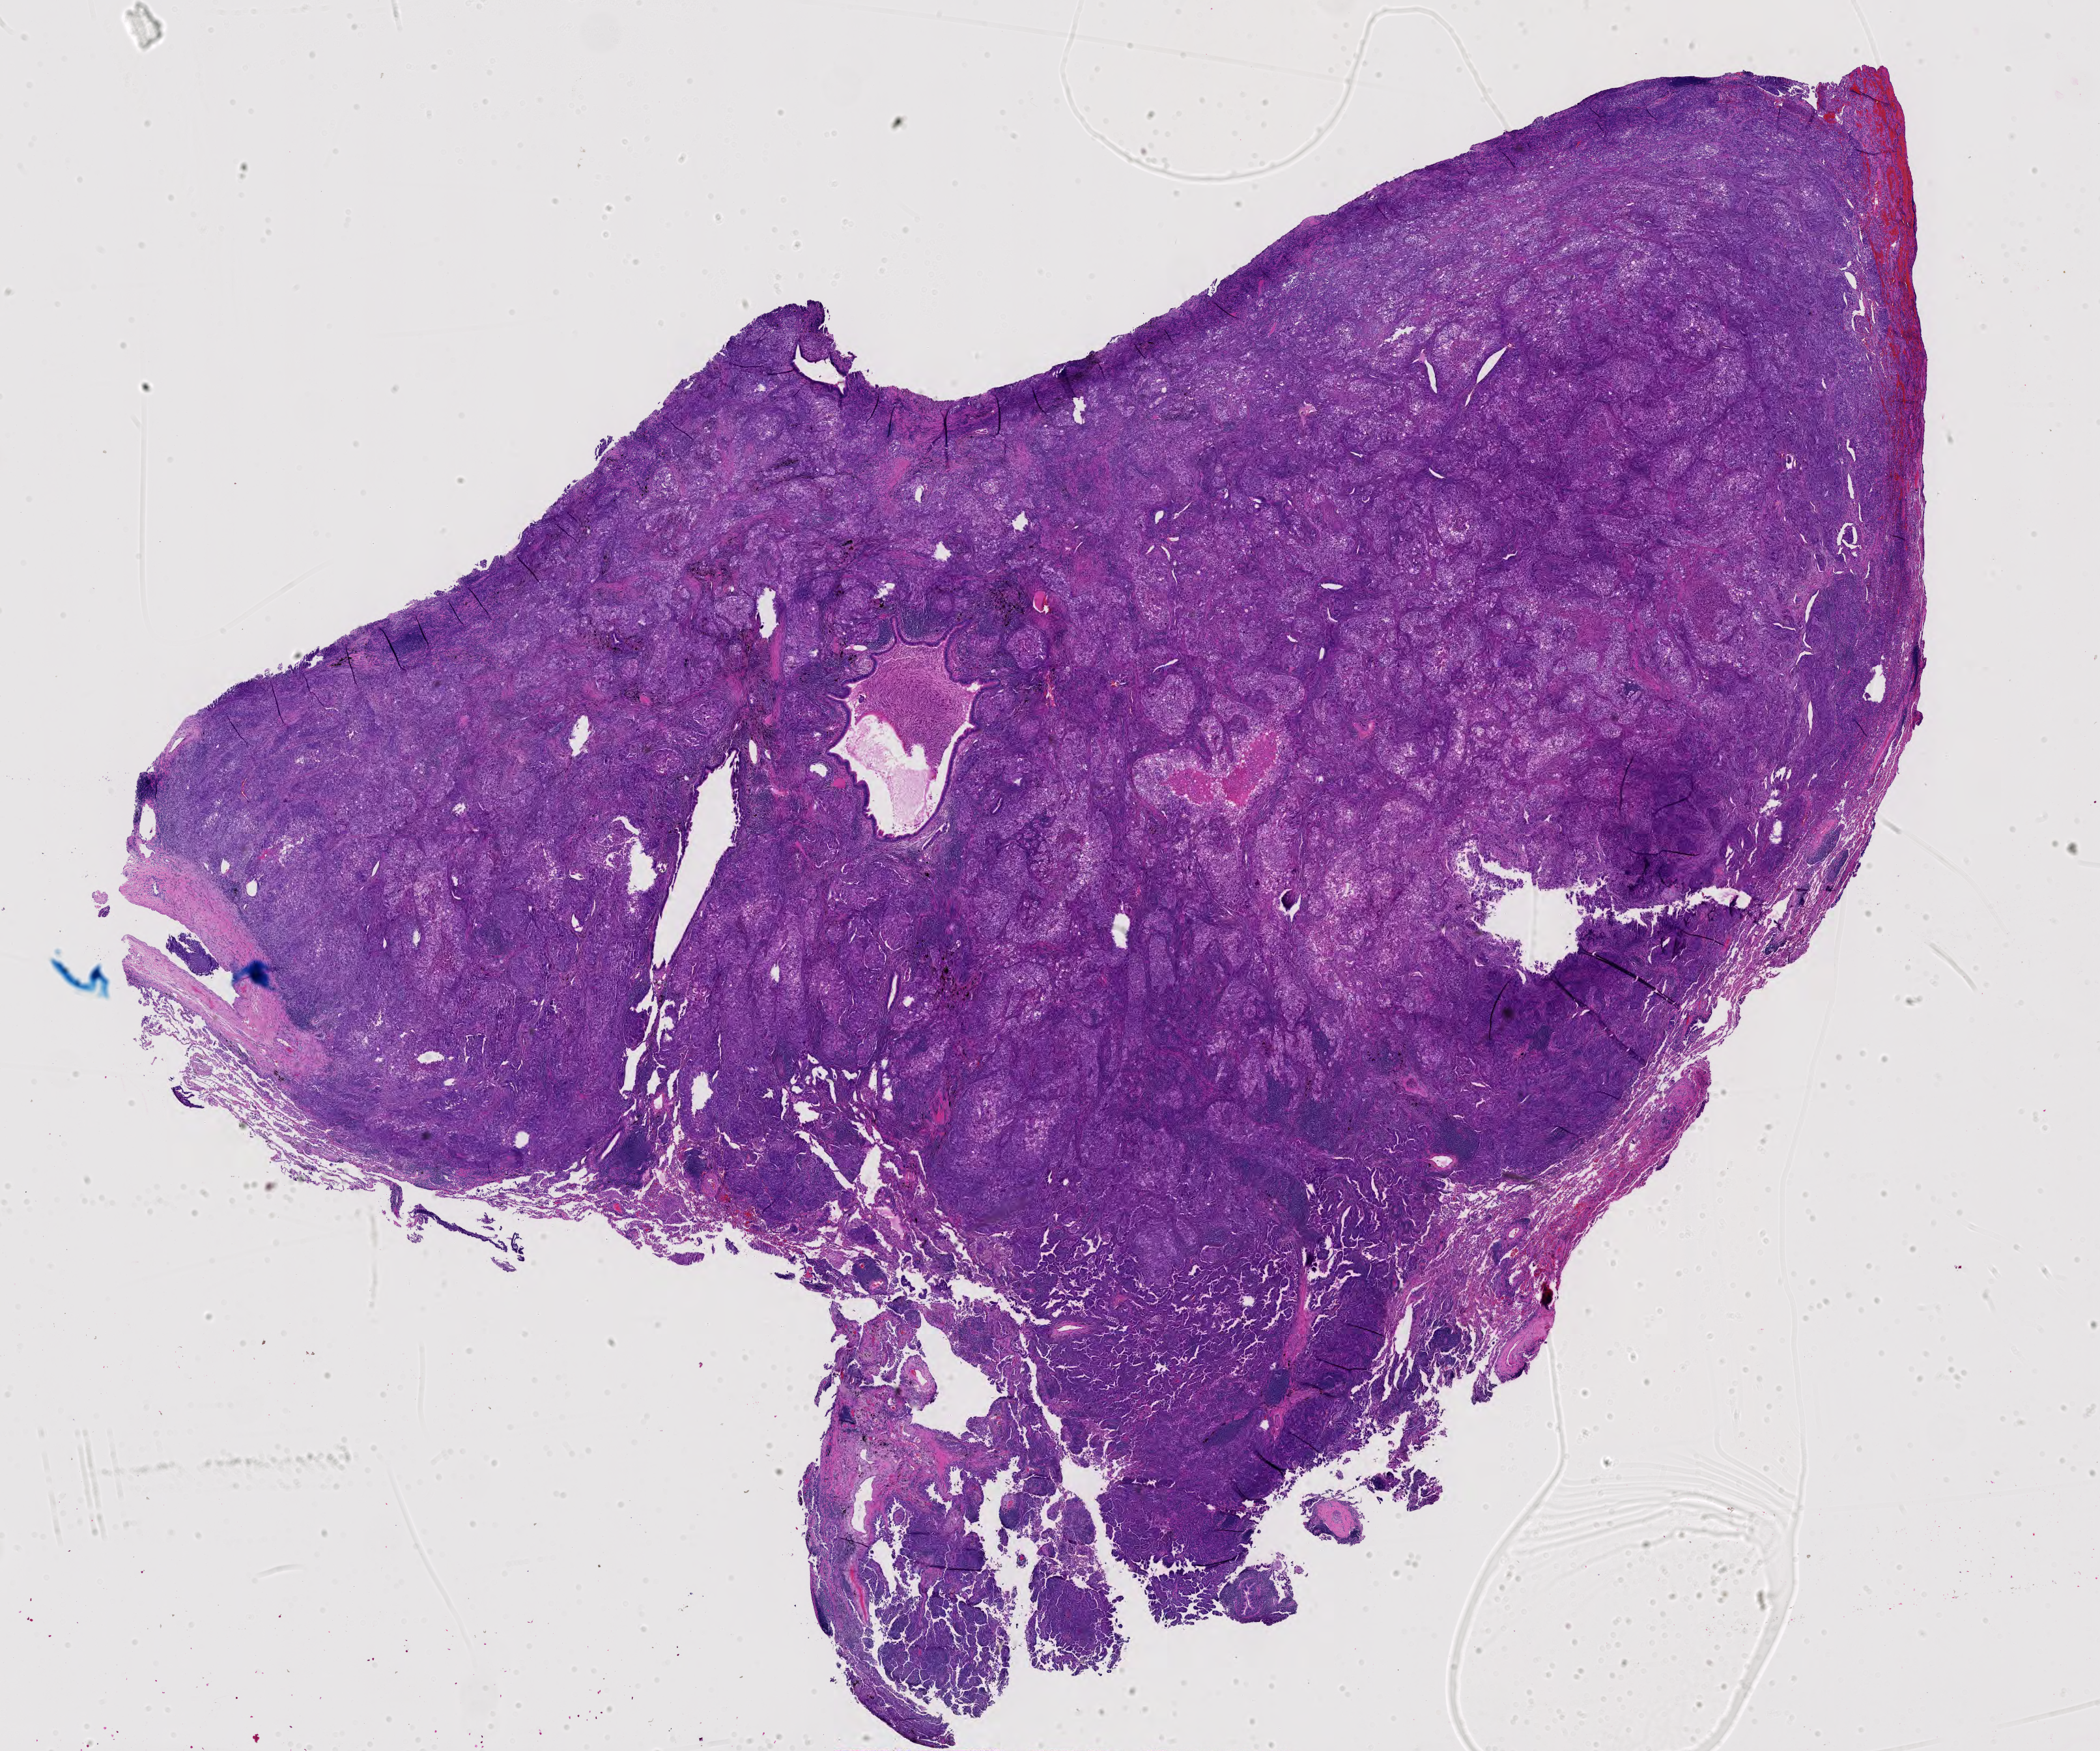
Whole-slide histology image, Hematoxylin and eosin (H&E) stained, shown as a low-resolution overview of the whole scanned area (about 23.4 x 19.5 mm, slide scanned at 40x); formalin-fixed paraffin-embedded (FFPE) diagnostic section; primary tumour sample from the lung. Female, age 62 years at initial diagnosis.
Histologic diagnosis: Adenocarcinoma, NOS.